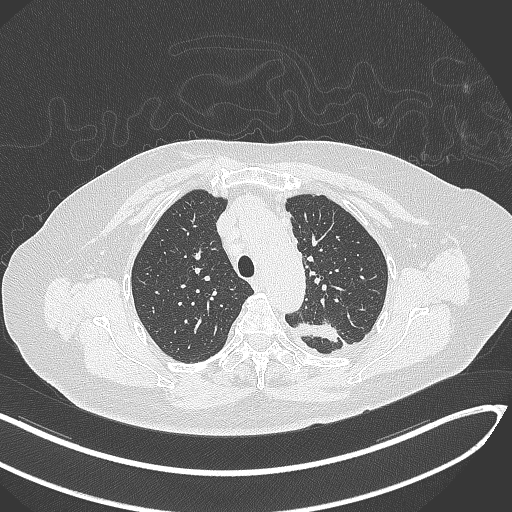
Chest CT, one axial slice. Slice 238 of 270 in the series (ordered by position). 120 kVp. Lung window (W 1500 / L -600 HU). 1 mm slice thickness. 512 × 512 image matrix, field of view 400 × 400 mm. Patient: female, 76 years. Case-level facts recorded for this patient, not image findings: clinical TNM (as recorded): T1c N0 M0.
Annotated regions visible in this slice (rectangle marked by the reading radiologist):
- lung tumour (recorded histology: adenocarcinoma): bounding box [x1, y1, x2, y2] px = [288, 318, 345, 349]